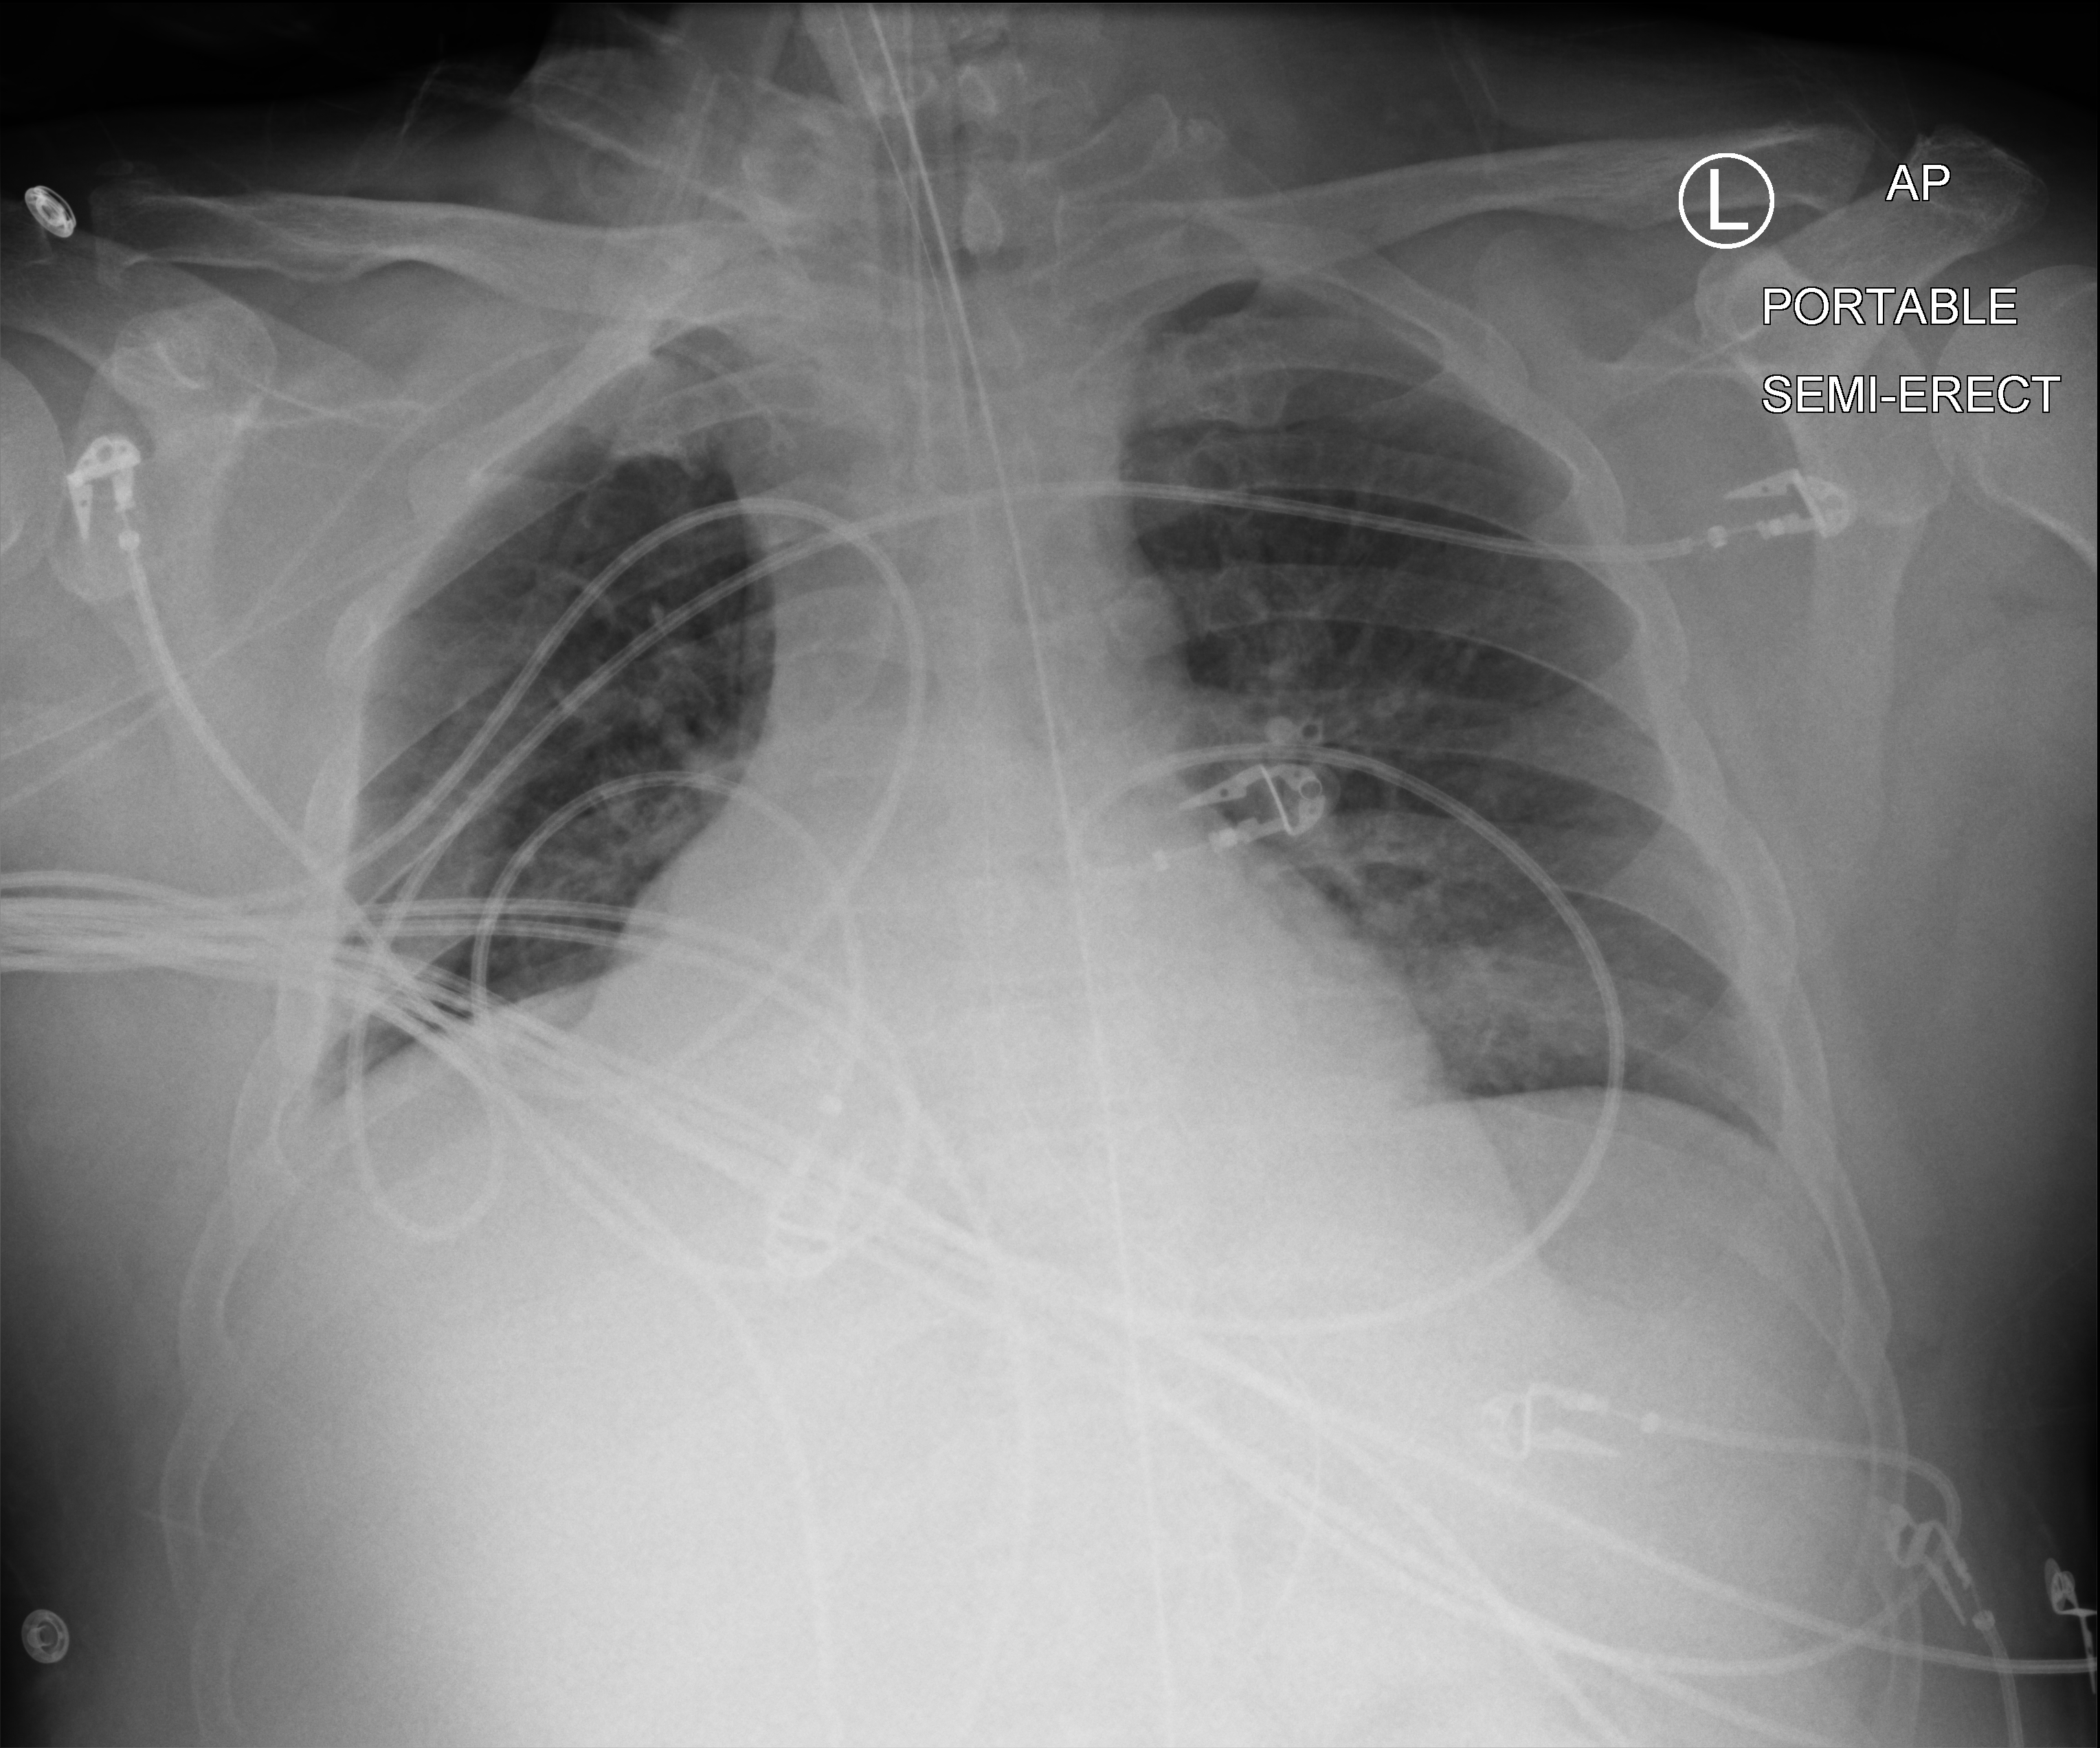
Portable chest radiograph; anteroposterior (AP) projection. Male patient hospitalised with COVID-19, age 18–59 years.
Hospital-stay facts (about this admission, not read from this image; timing relative to this image not recorded): mechanically ventilated during this hospital stay: yes.